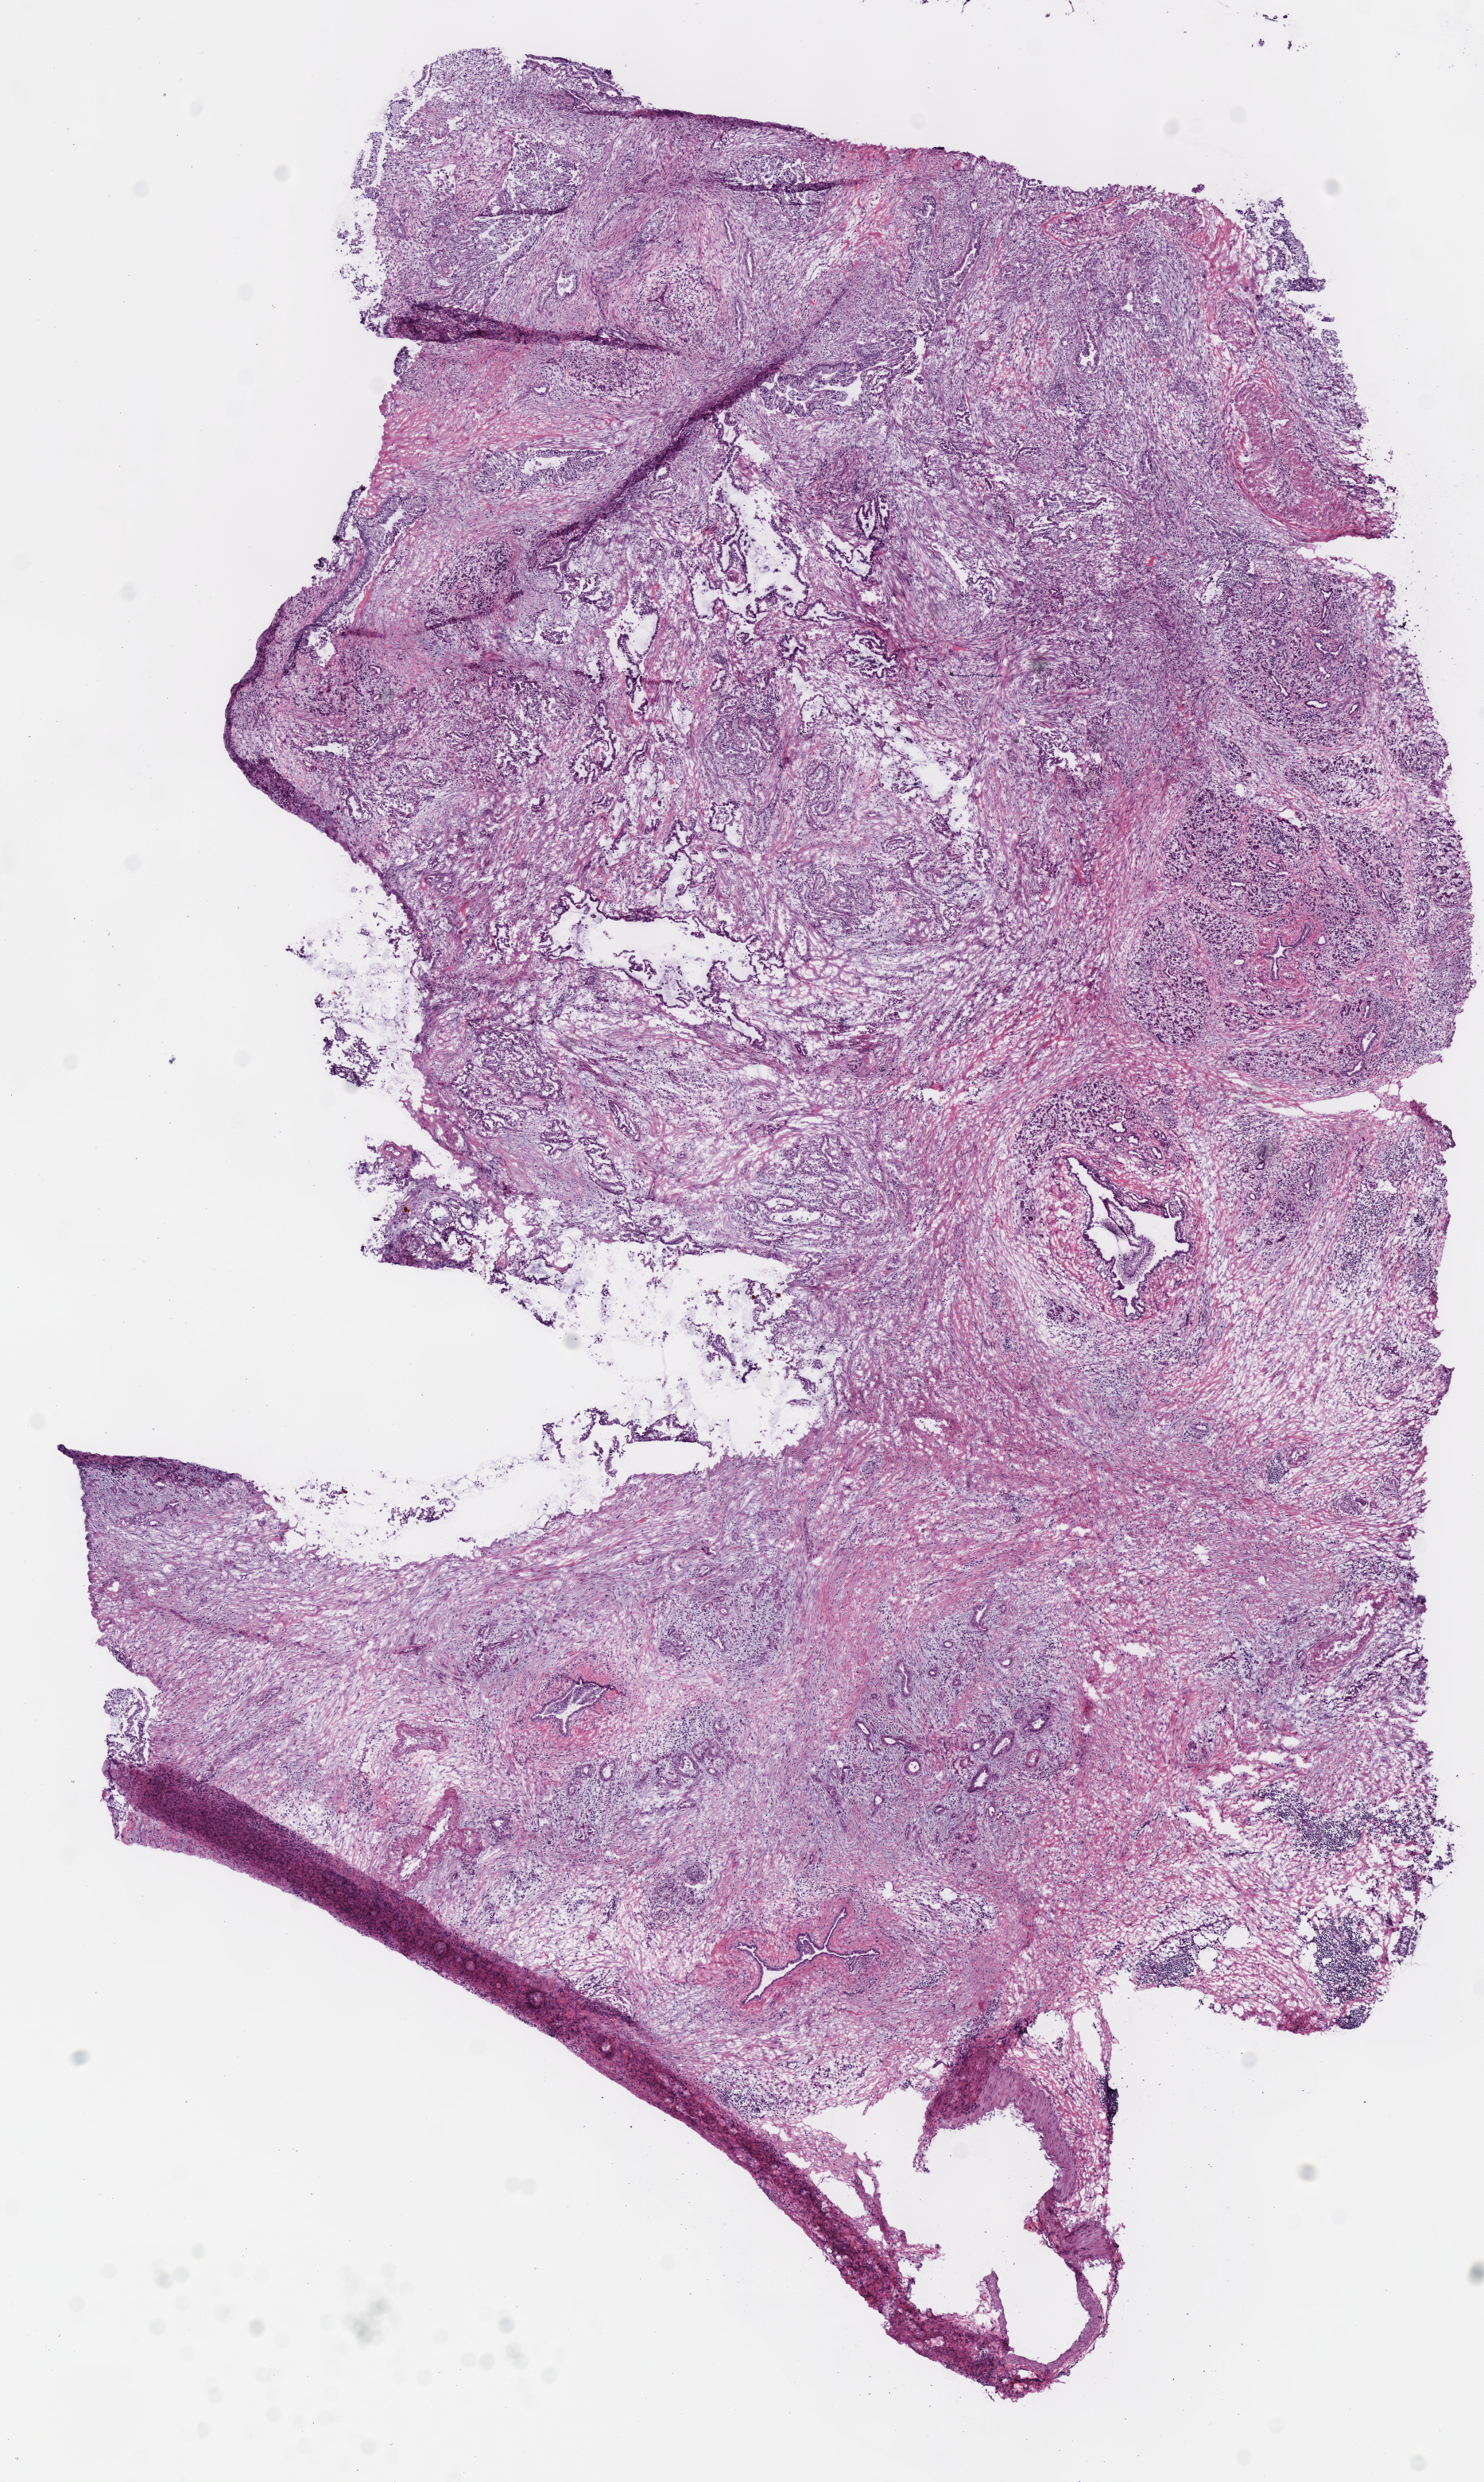
Digitized H&E-stained tissue section (whole slide), low-resolution overview of the scanned area, about 7.3 x 12.3 mm. Frozen section from the top of the tissue portion. Pancreas, primary tumour sample. Patient: female, age at initial diagnosis 54 years. Histologic grade: G2 (moderately differentiated). Pathologist review of this section (percent, as recorded): tumour cells 50%, tumour nuclei 50%, normal cells 20%, stromal cells 30%, necrosis 0%.
- histologic diagnosis: Infiltrating duct carcinoma, NOS (head of pancreas)
- AJCC pathologic stage: IIA (7th edition)